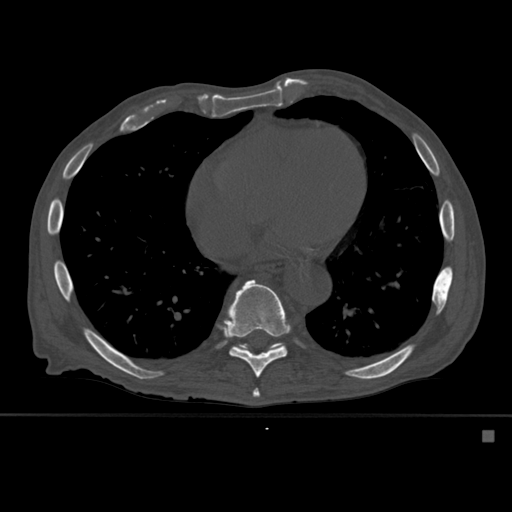
CT including the spine, one axial slice. Bone window (W 1800 / L 400 HU). 512 × 512 image matrix. Patient: male, 78 years. Case-level facts recorded for this patient, not image findings: primary cancer: prostate.
Annotated regions visible in this slice (semi-automatic segmentation, software-assisted and operator-edited):
- T10 vertebra: bounding box (x1, y1, x2, y2) in pixels: (236, 344, 278, 350)
- T8 vertebra: (252, 389, 260, 398)
- T9 vertebra: (222, 279, 292, 378)